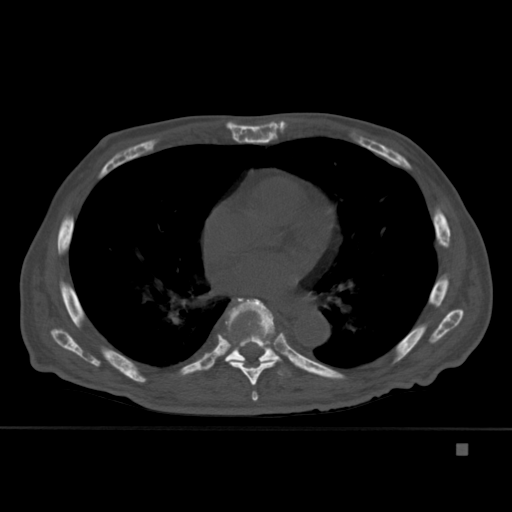
CT including the spine, one axial slice; slice 273 of 451 in the series (ordered by position); bone window (W 1800 / L 400 HU); 512 × 512 image matrix, field of view 378 × 378 mm. Patient: male, 75 years. From the clinical record (not read from this slice): primary cancer: prostate.
Annotated regions visible in this slice (semi-automatic segmentation, software-assisted and operator-edited):
- T6 vertebra: bounding box <252,391,259,401> (left, top, right, bottom; pixels)
- T7 vertebra: <224,298,282,386>
- T8 vertebra: <225,298,289,376>